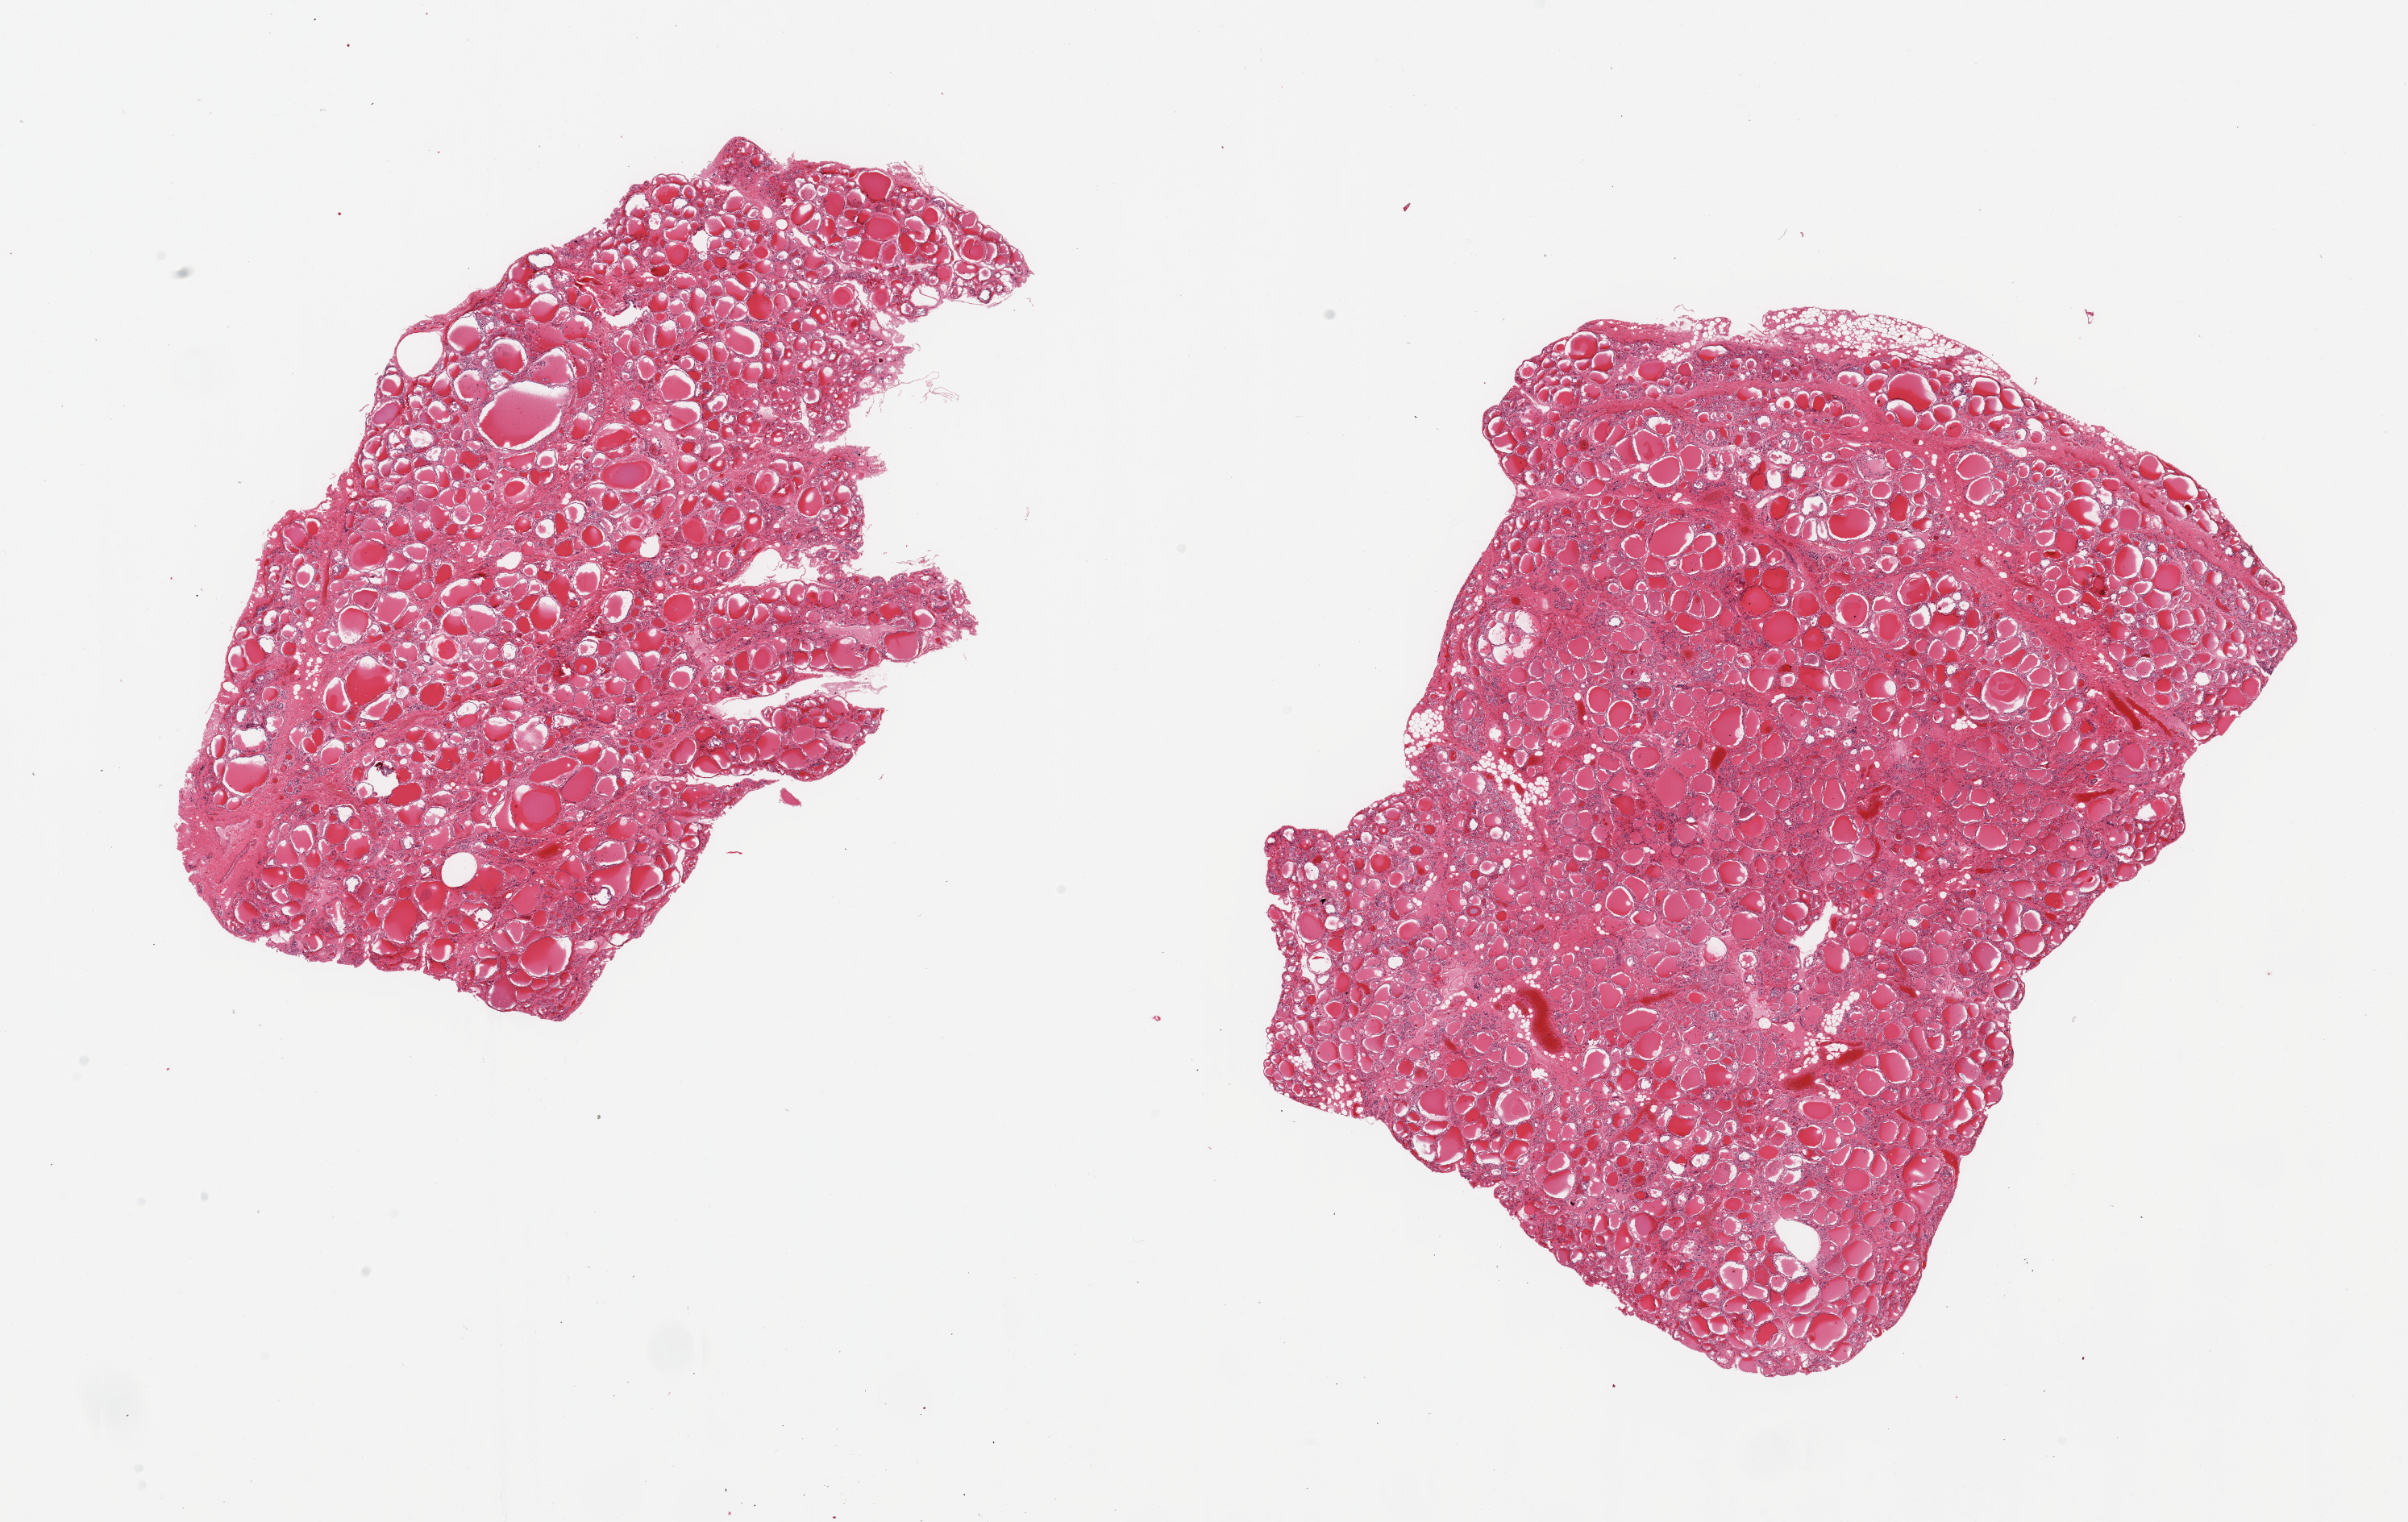
Whole-slide image, hematoxylin and eosin (H&E) stain, a low-resolution overview of the entire scanned area, about 23.6 x 14.9 mm; PAXgene-fixed paraffin-embedded (PFPE) section; sampled site (target tissue): thyroid; donor tissue sample. Donor sex: female.
* review note (as recorded): 2 pieces, no abnormalities